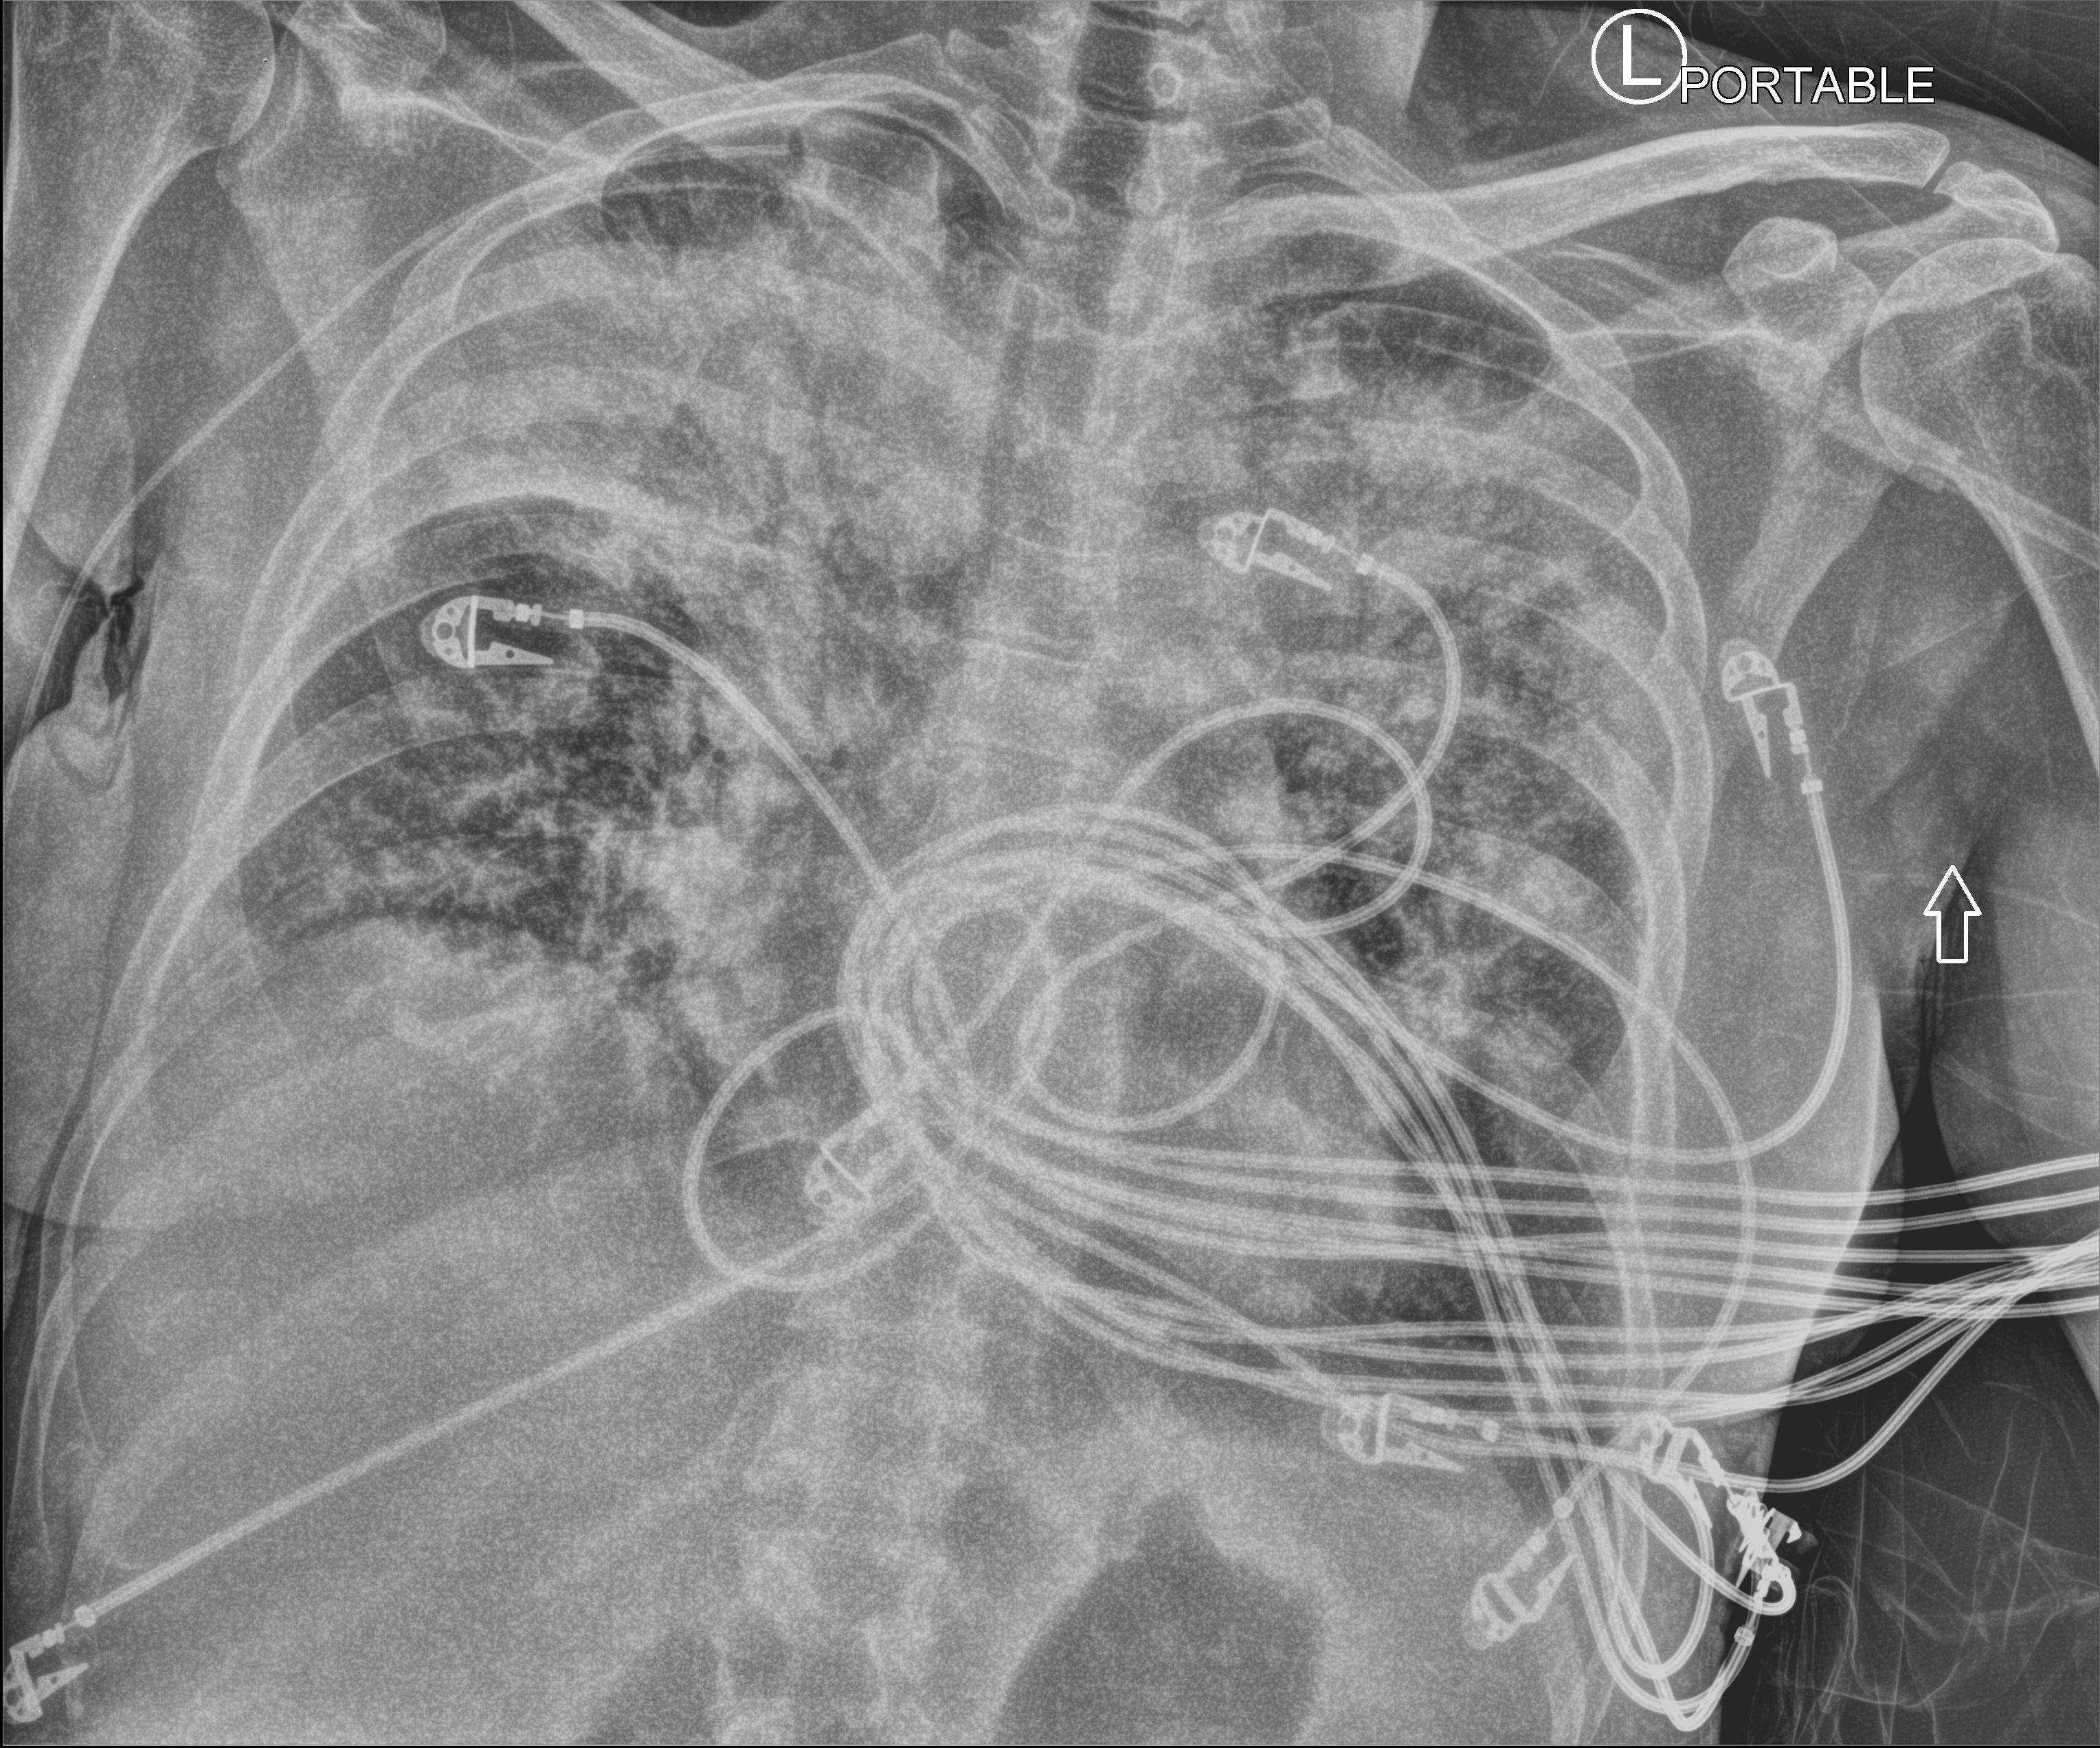
Bedside chest radiograph (computed radiography). Female patient hospitalised with COVID-19, age 18–59 years.
Hospital-stay facts (about this admission, not read from this image; timing relative to this image not recorded): smoking status (admission record): never; mechanically ventilated during this hospital stay: no.